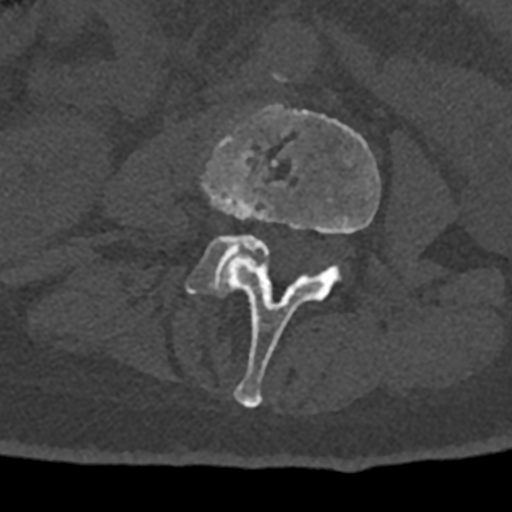
CT including the spine, one axial slice. Position 303 of 797 along the scan axis. 120 kVp. Bone window (W 1800 / L 400 HU). 512 × 512 image matrix, field of view 160 × 160 mm. Male patient, age 74 years. Case-level facts recorded for this patient, not image findings: primary cancer: renal; vertebrae with lytic lesions (as recorded): T10, L1, L2, L3, L4, L5.
Outlined on this slice (semi-automatically segmented with operator editing):
- L3 vertebra: bounding box [x1, y1, x2, y2] px = [201, 105, 381, 408]
- L4 vertebra: [185, 234, 270, 297]